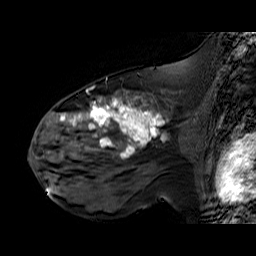
Breast MRI (dynamic contrast-enhanced), one sagittal slice; slice 36 of 60 in the series (ordered by position); dynamic contrast-enhanced series, time point 2 of 6 at this slice position (early post-contrast); 1.5 T; TE 6.3 ms, TR 32.9 ms; 4 mm slice thickness; 256 × 256 image matrix, field of view 200 × 200 mm. Female patient. From the clinical record (not read from this slice): setting: breast cancer imaged before/during neoadjuvant chemotherapy; receptor status: HER2-positive.
Structures marked on this image (semi-automatic segmentation, software-assisted and operator-edited):
- analysis volume of interest (the breast-tissue region the enhancement analysis was run in; not a lesion): bounding box [x1, y1, x2, y2] px = [48, 92, 195, 174]
- tumour enhancement mask (voxels above the 100 % enhancement threshold inside the analysis volume of interest): [60, 96, 166, 158]